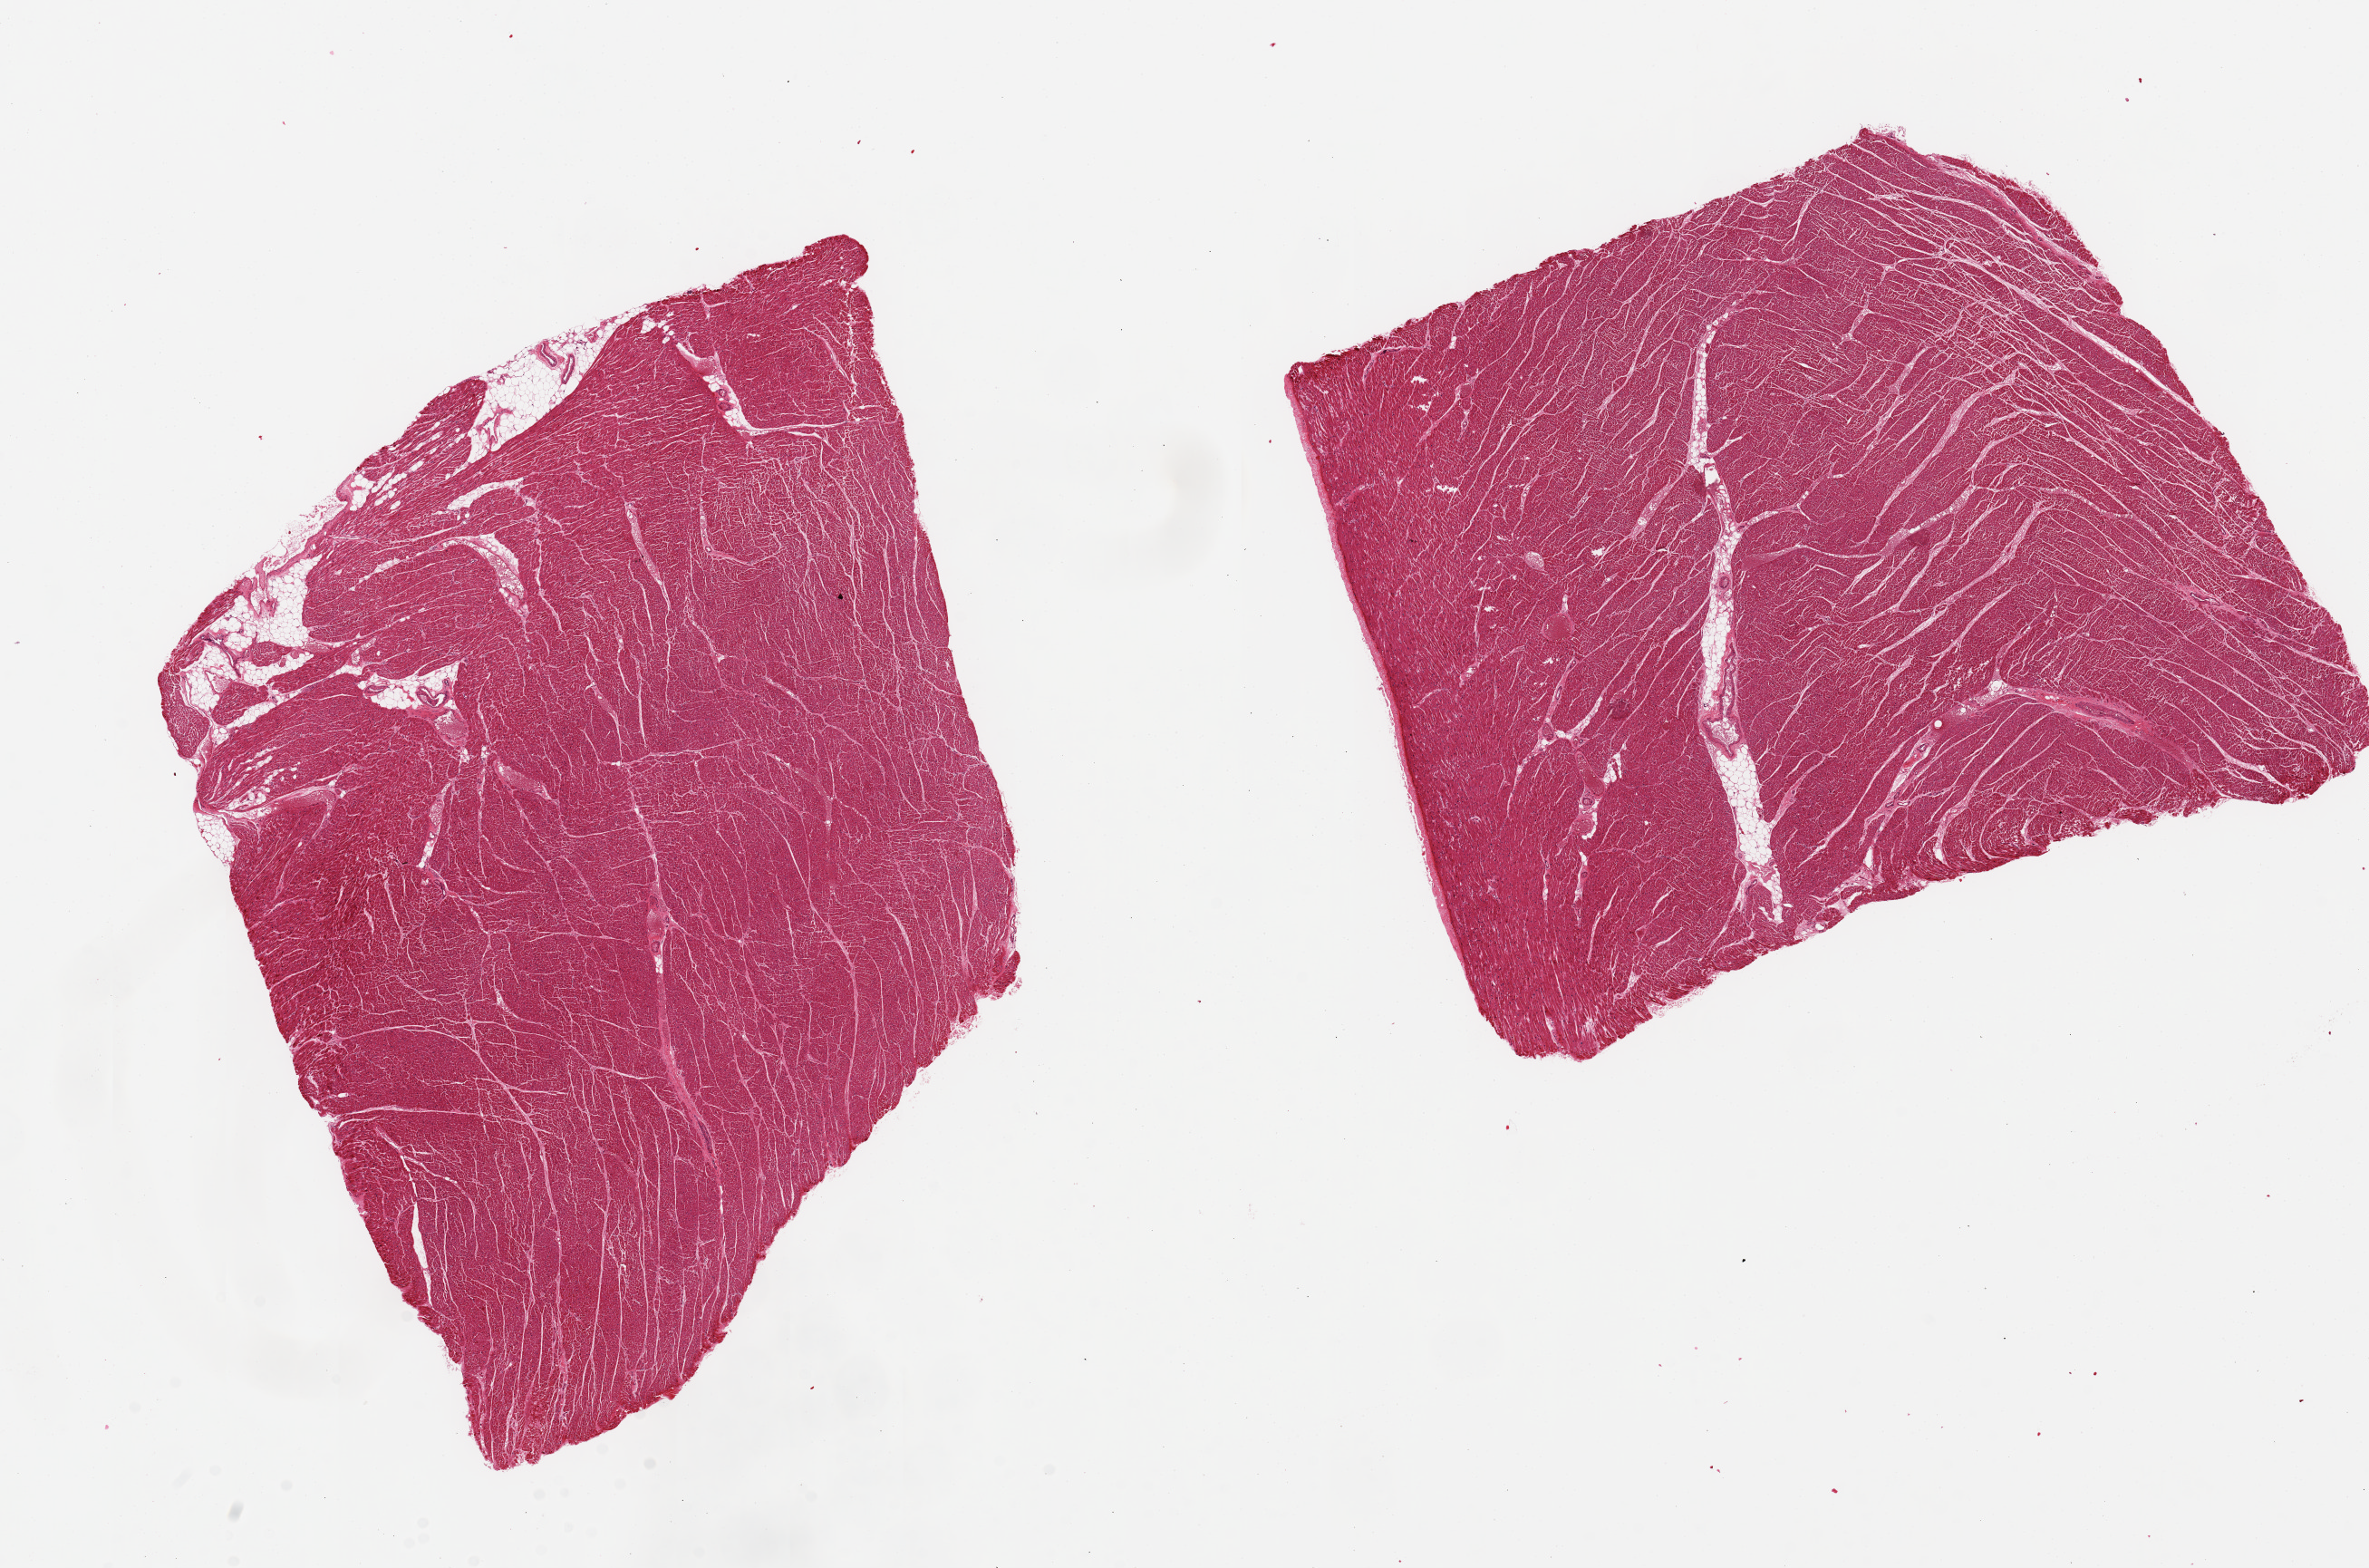
Hematoxylin and eosin (H&E) whole-slide image, a low-resolution overview of the entire scanned area, about 20.7 x 13.7 mm. PAXgene-fixed paraffin-embedded (PFPE) section. Section of heart (target tissue). Donor tissue sample. Donor sex: male.
Pathologist's review note for this sample: 2 pieces 8x6.8 mm; early ischemic changes; <5% embedded fat.